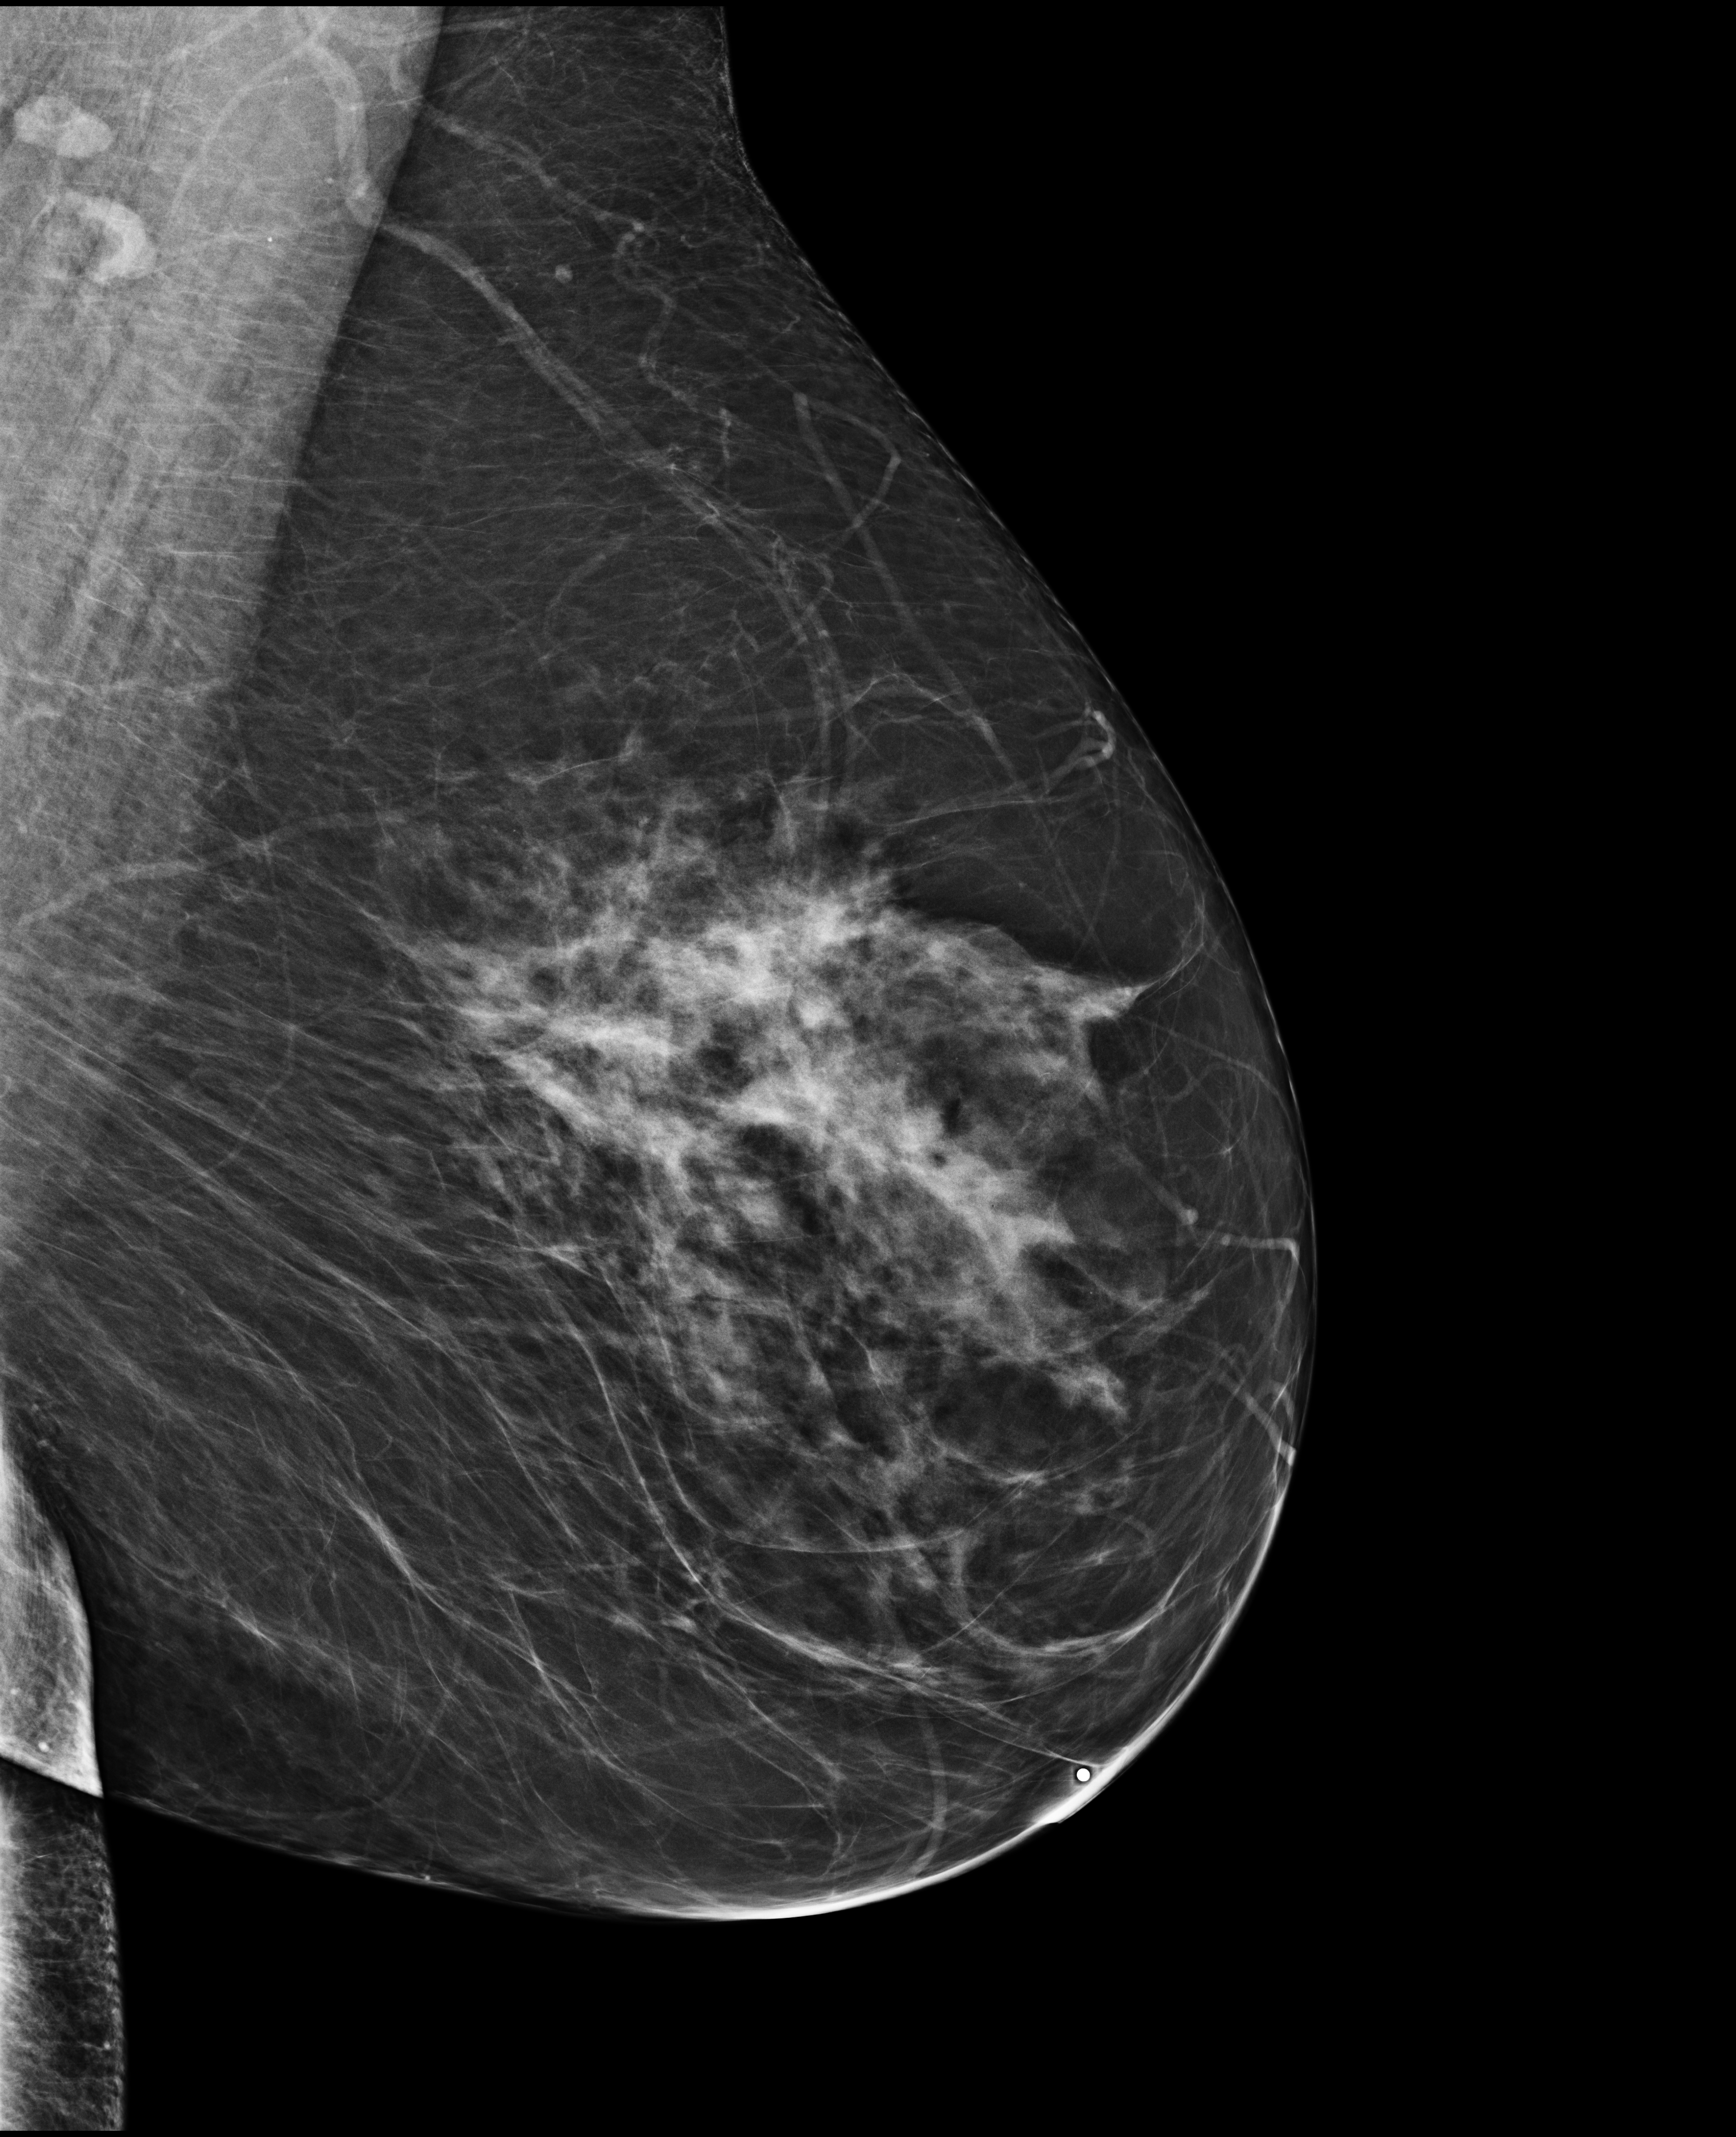
Screening examination; system: Selenia Dimensions. Patient: female, 61 years.
Image type: full-field digital mammogram. Breast: left. Projection: mediolateral oblique (MLO) view.